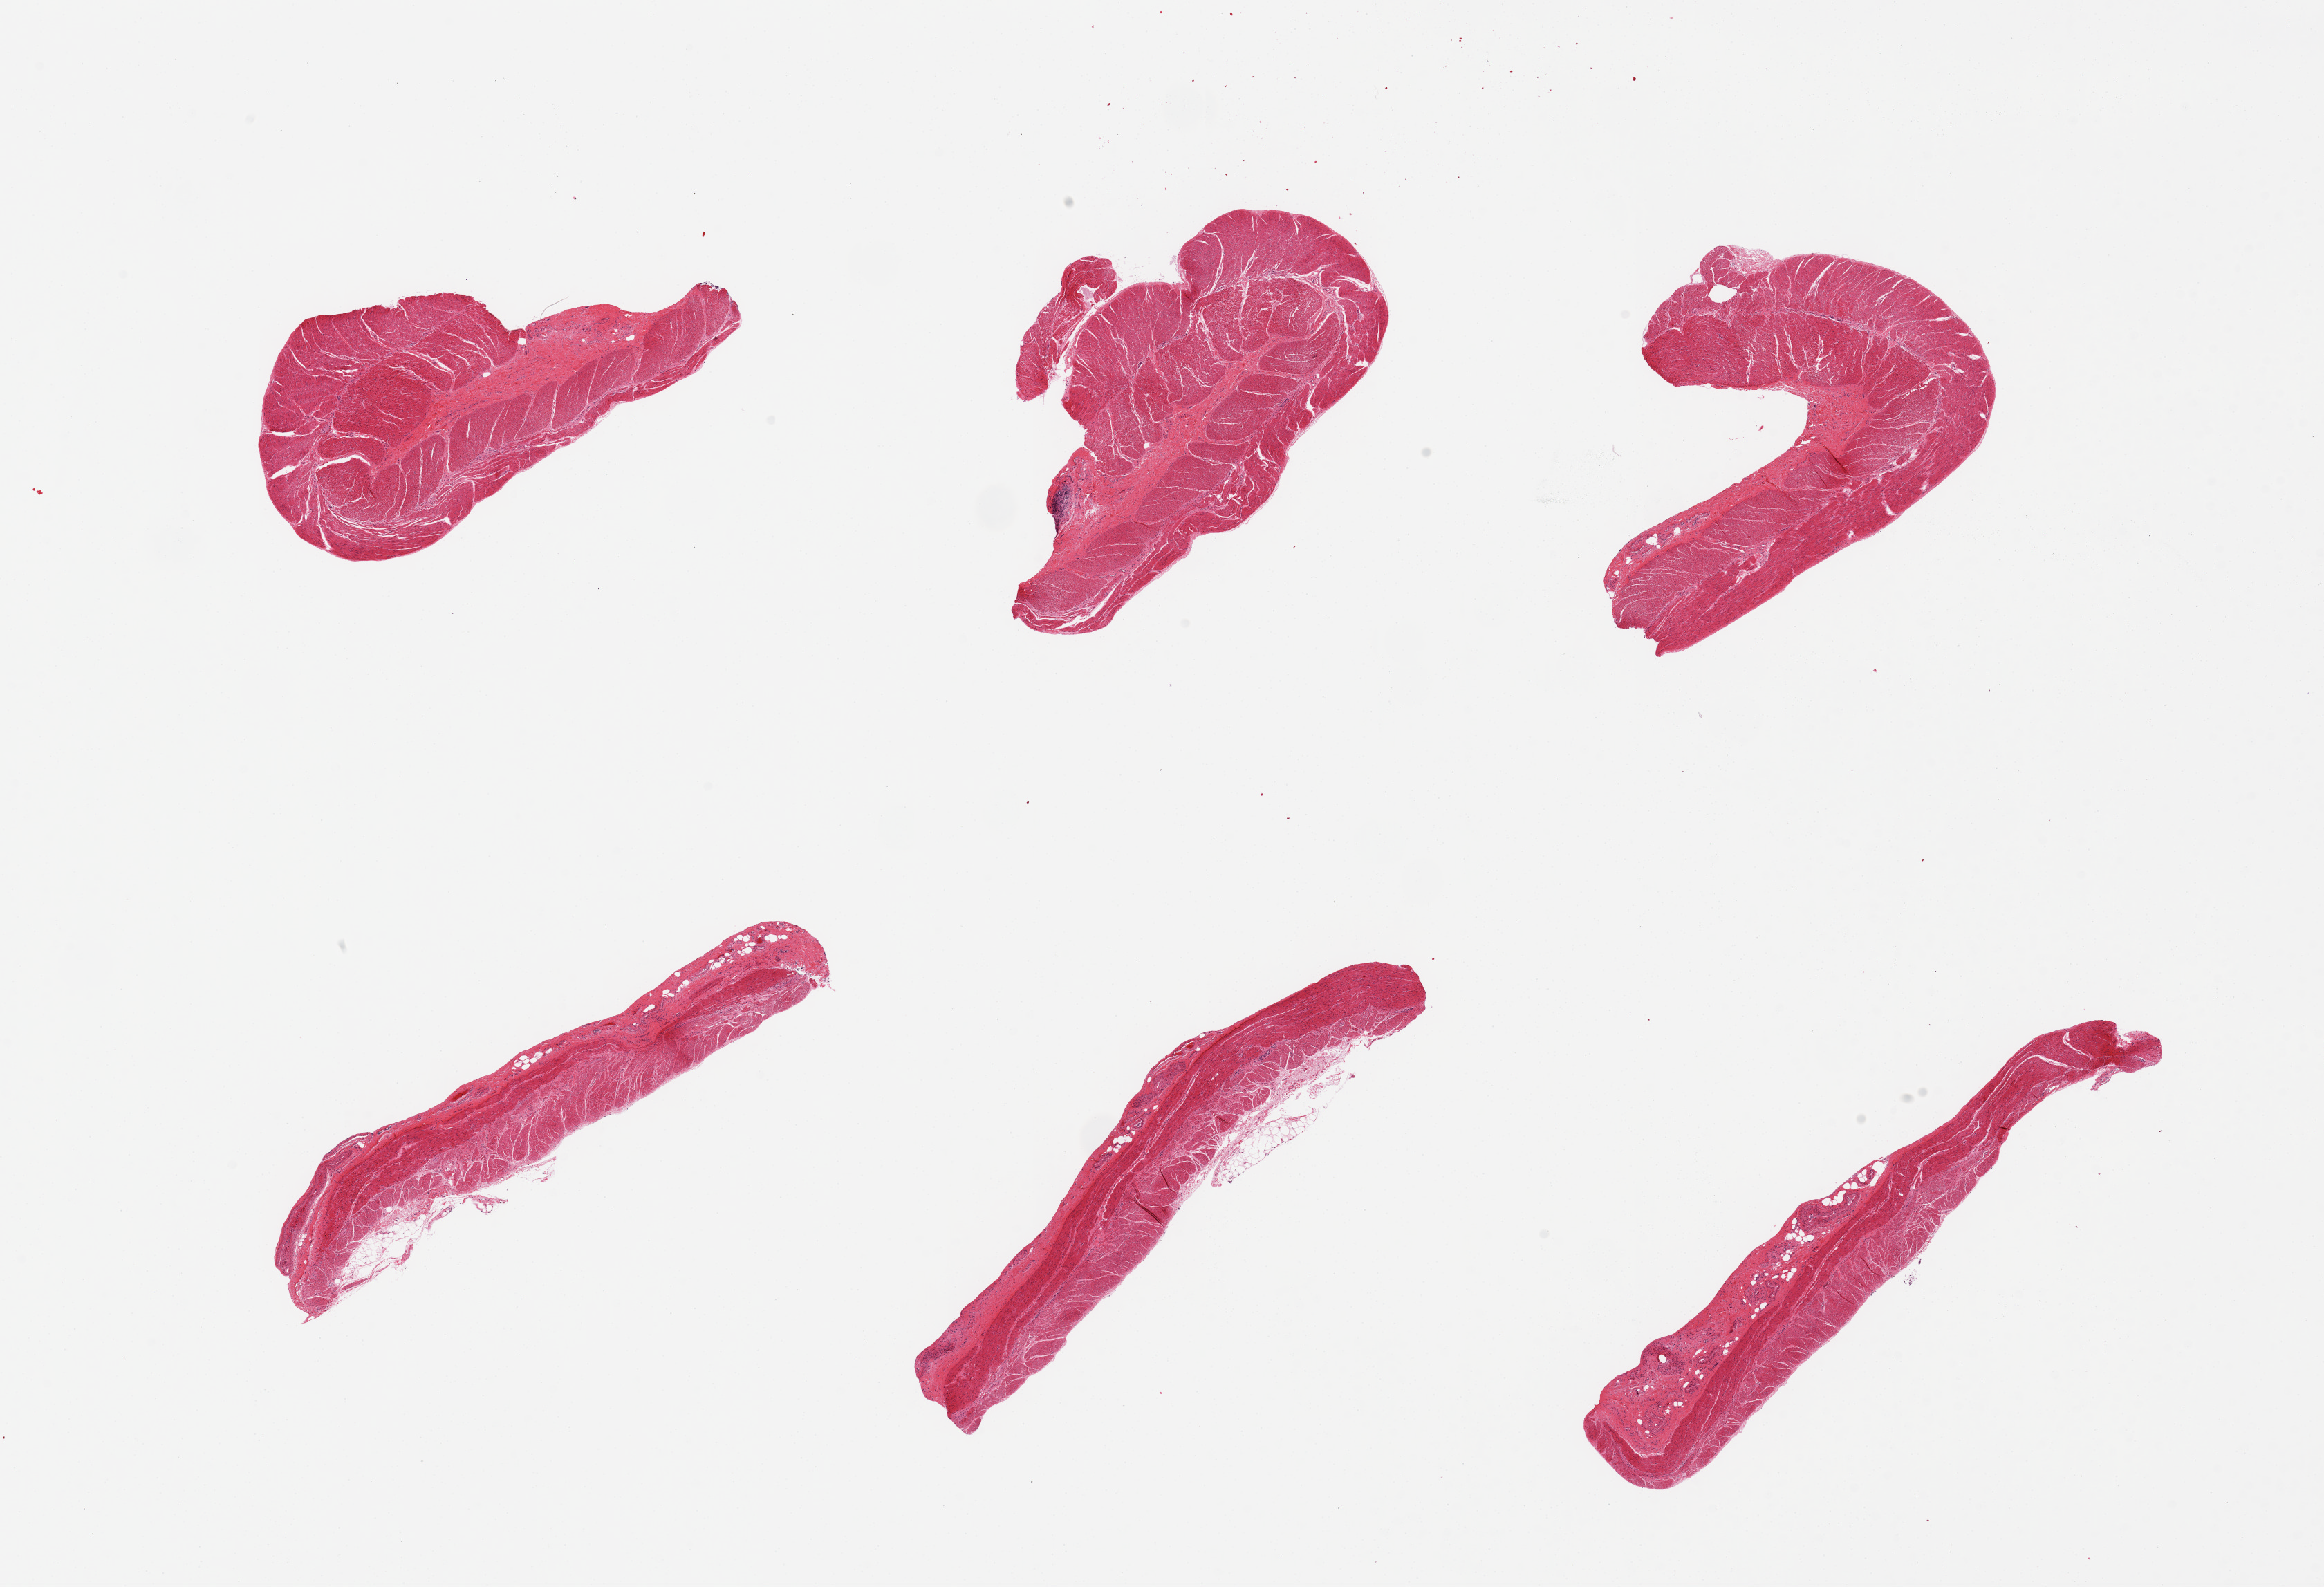
Hematoxylin and eosin (H&E) whole-slide image — whole scanned area (about 26.6 x 18.1 mm, acquisition: 20x scan) shown as a low-resolution overview; PAXgene-fixed, paraffin-embedded tissue; sampled site (target tissue): sigmoid colon; tissue donor sample. Donor: female.
Review note (as recorded): 6 pieces, all muscularis, good specimens.